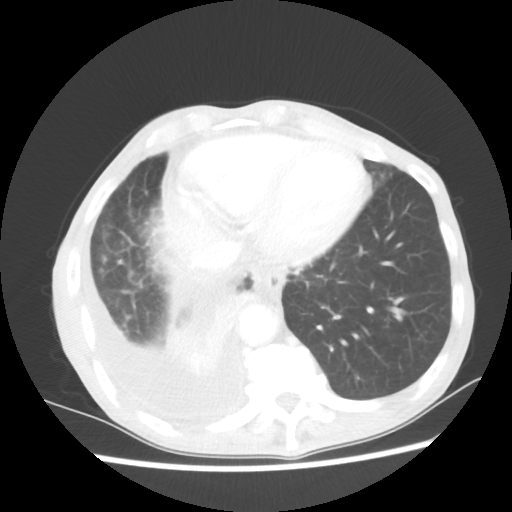
Chest CT, one axial slice; position 16 of 60 along the scan axis; lung window (W 1500 / L -600 HU); 5 mm slice thickness; 512 × 512 image matrix, field of view 335 × 335 mm. Male patient, age 76 years. From the clinical record (not read from this slice): clinical TNM (as recorded): T3 N3 M1a; histopathological grade: G3.
Annotated regions visible in this slice (rectangle marked by the reading radiologist):
- lung tumour (recorded histology: squamous cell carcinoma): bounding box [x1, y1, x2, y2] px = [152, 287, 260, 389]